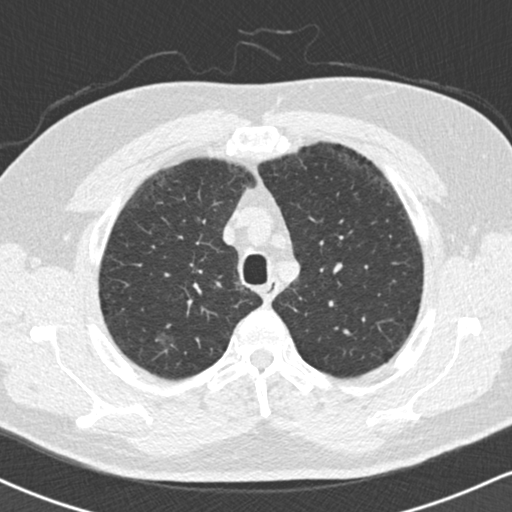
Axial slice from a low-dose chest CT screening exam, second annual screen, lung window (W 1500 / L -600 HU), standard (soft-tissue) reconstruction kernel (B30f), 120 kVp, slice 37 of 169 in the series. Male, age 59 years at enrolment. Current smoker at enrolment.
Expert-annotated lung lesion, bounding box <151,315,201,366> (left, top, right, bottom; pixels). The exam's reader record, not a measurement of the box and not confirmed to be the same lesion: non-calcified nodule or mass ≥4 mm, right upper lobe, 18 × 16 mm, ground glass attenuation, pre-existing on the prior screen: yes. Official screen result: positive, no significant change: stable abnormalities potentially related to lung cancer, unchanged since the prior screening exam. Lung cancer was diagnosed 60 days after this screen: bronchiolo-alveolar adenocarcinoma, NOS, right lower lobe, stage IA (AJCC 6th edition), 15 mm at pathology.